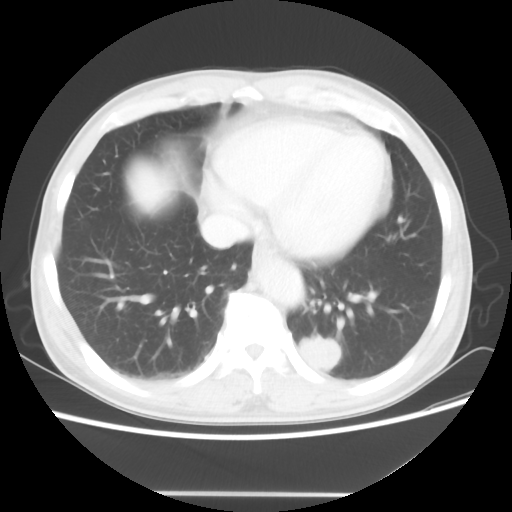
Chest CT, one axial slice; slice 17 of 60 in the series (ordered by position); reconstruction kernel STANDARD; lung window (W 1500 / L -600 HU); 512 × 512 image matrix, field of view 360 × 360 mm. Male patient, age 55 years. From the clinical record (not read from this slice): clinical TNM (as recorded): T1c N3 M0; histopathological grade: G3.
Annotated regions visible in this slice (bounding box drawn by a radiologist):
- lung tumour (recorded histology: small cell carcinoma): bounding box <296,329,349,376> (left, top, right, bottom; pixels)